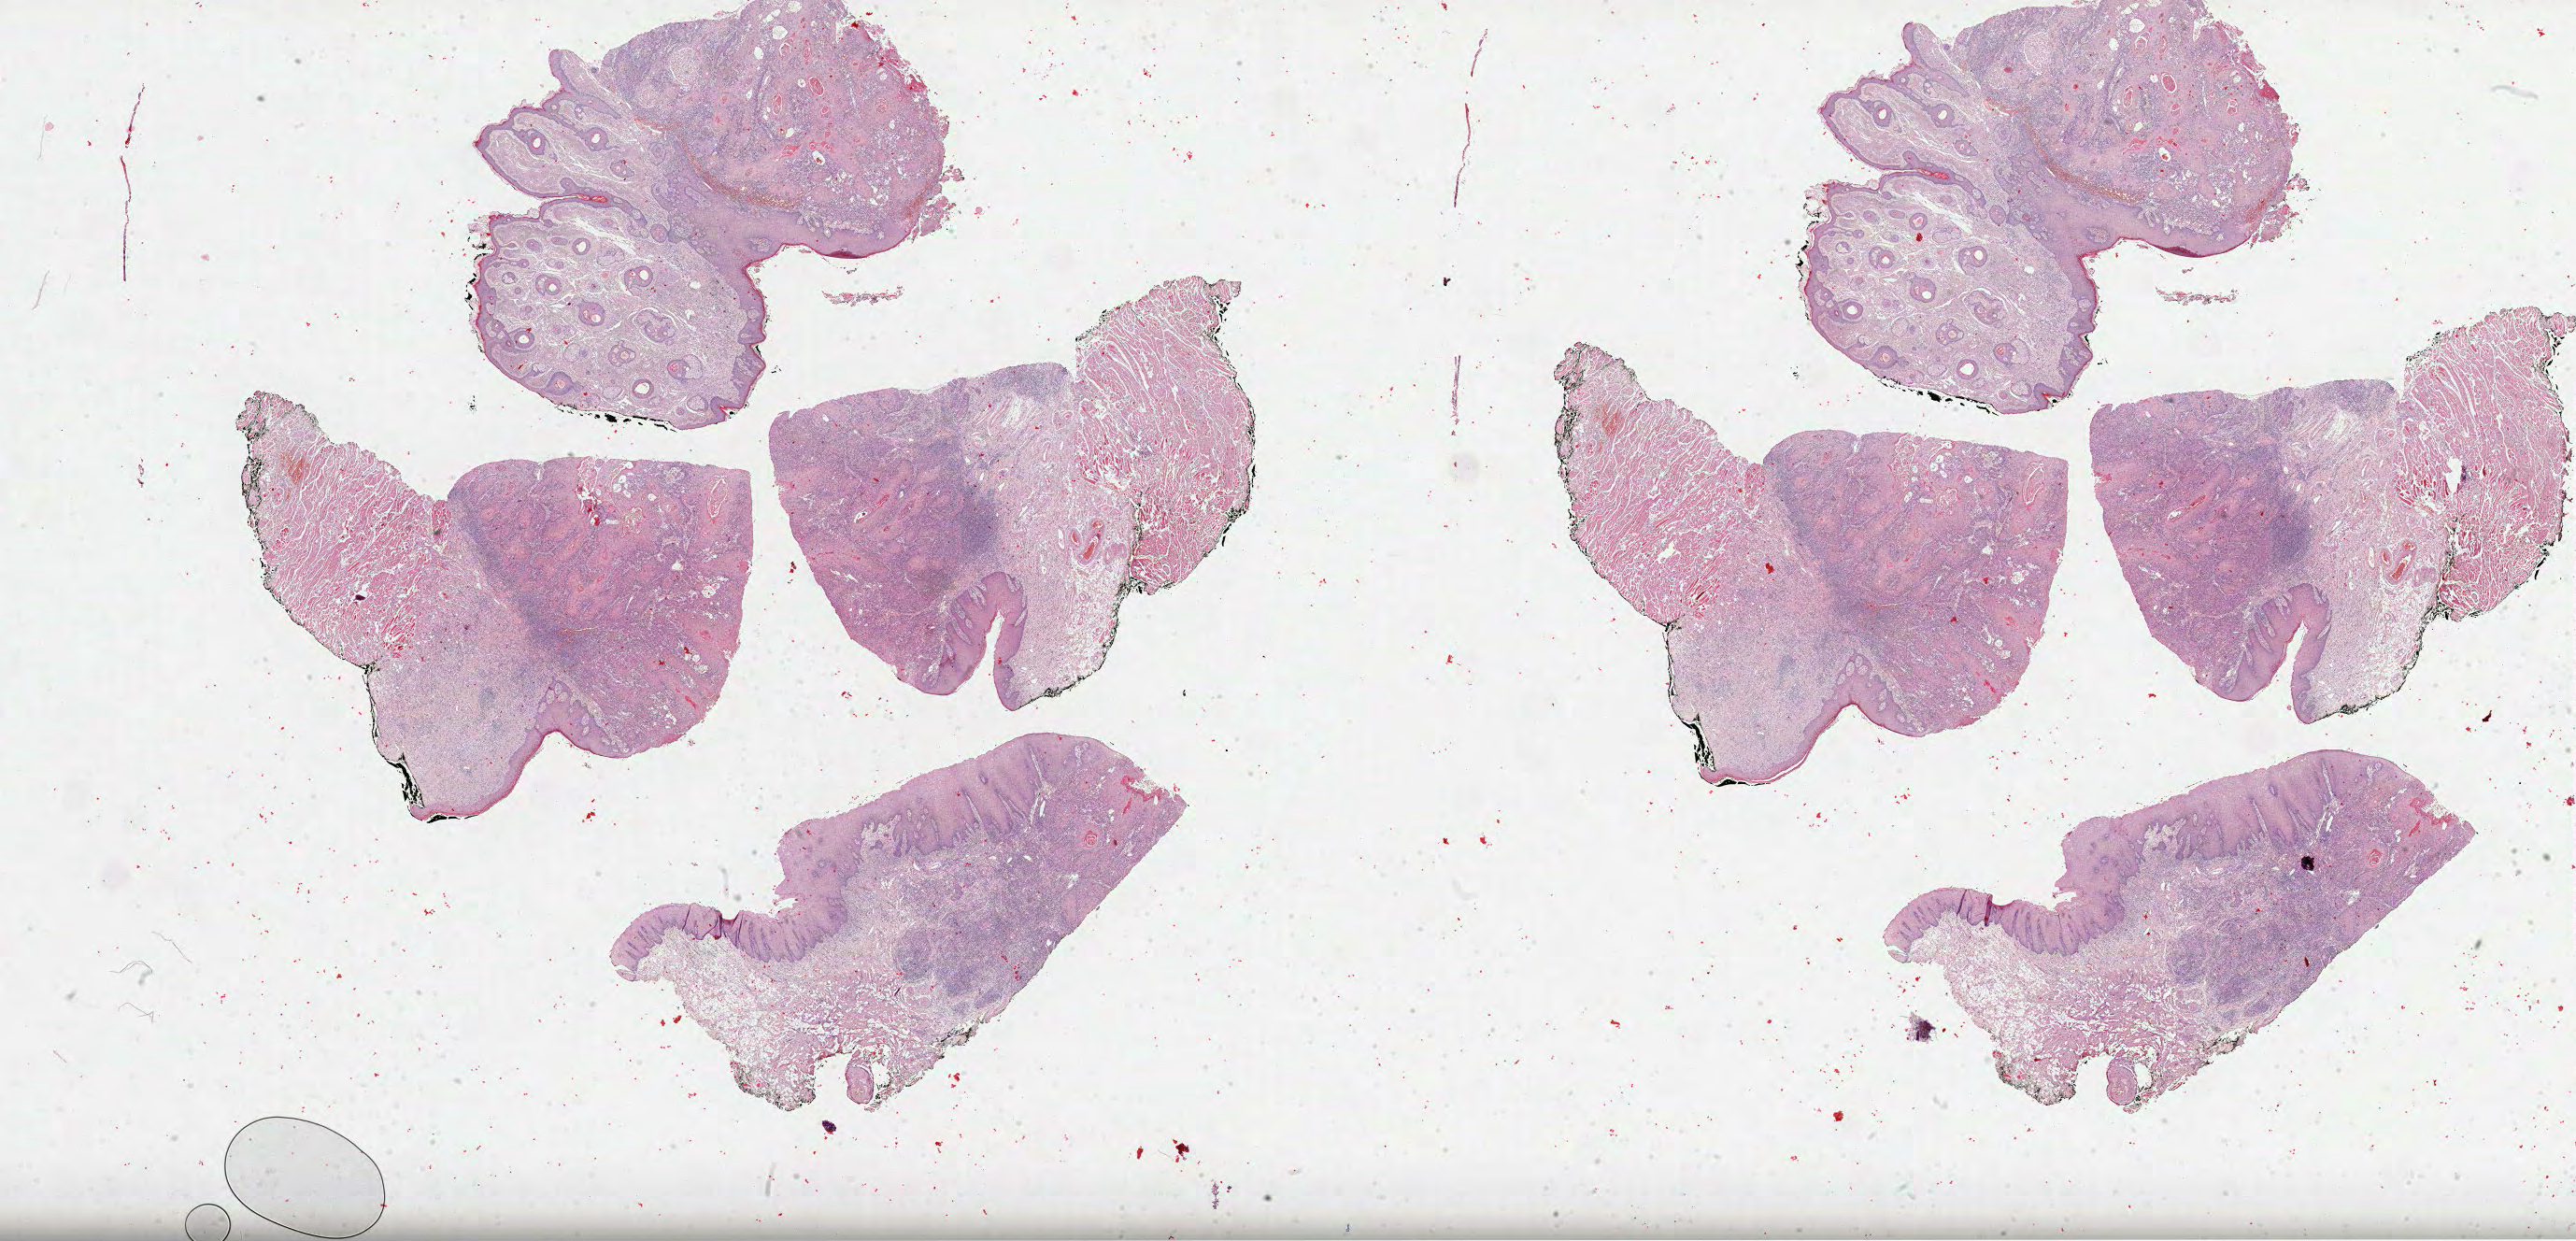
Whole-slide histology image, H&E-stained, shown as a low-resolution overview of the whole scanned area (about 44.5 x 21.4 mm, slide scanned at 40x). Formalin-fixed paraffin-embedded (FFPE) diagnostic section. Head and neck, primary tumour sample. Male patient; age at initial diagnosis 69 years. Histologic grade: G2 (moderately differentiated).
AJCC pathologic stage: I (7th edition). Pathologic diagnosis: Squamous cell carcinoma, NOS (lip, NOS). TNM: T1 N0.